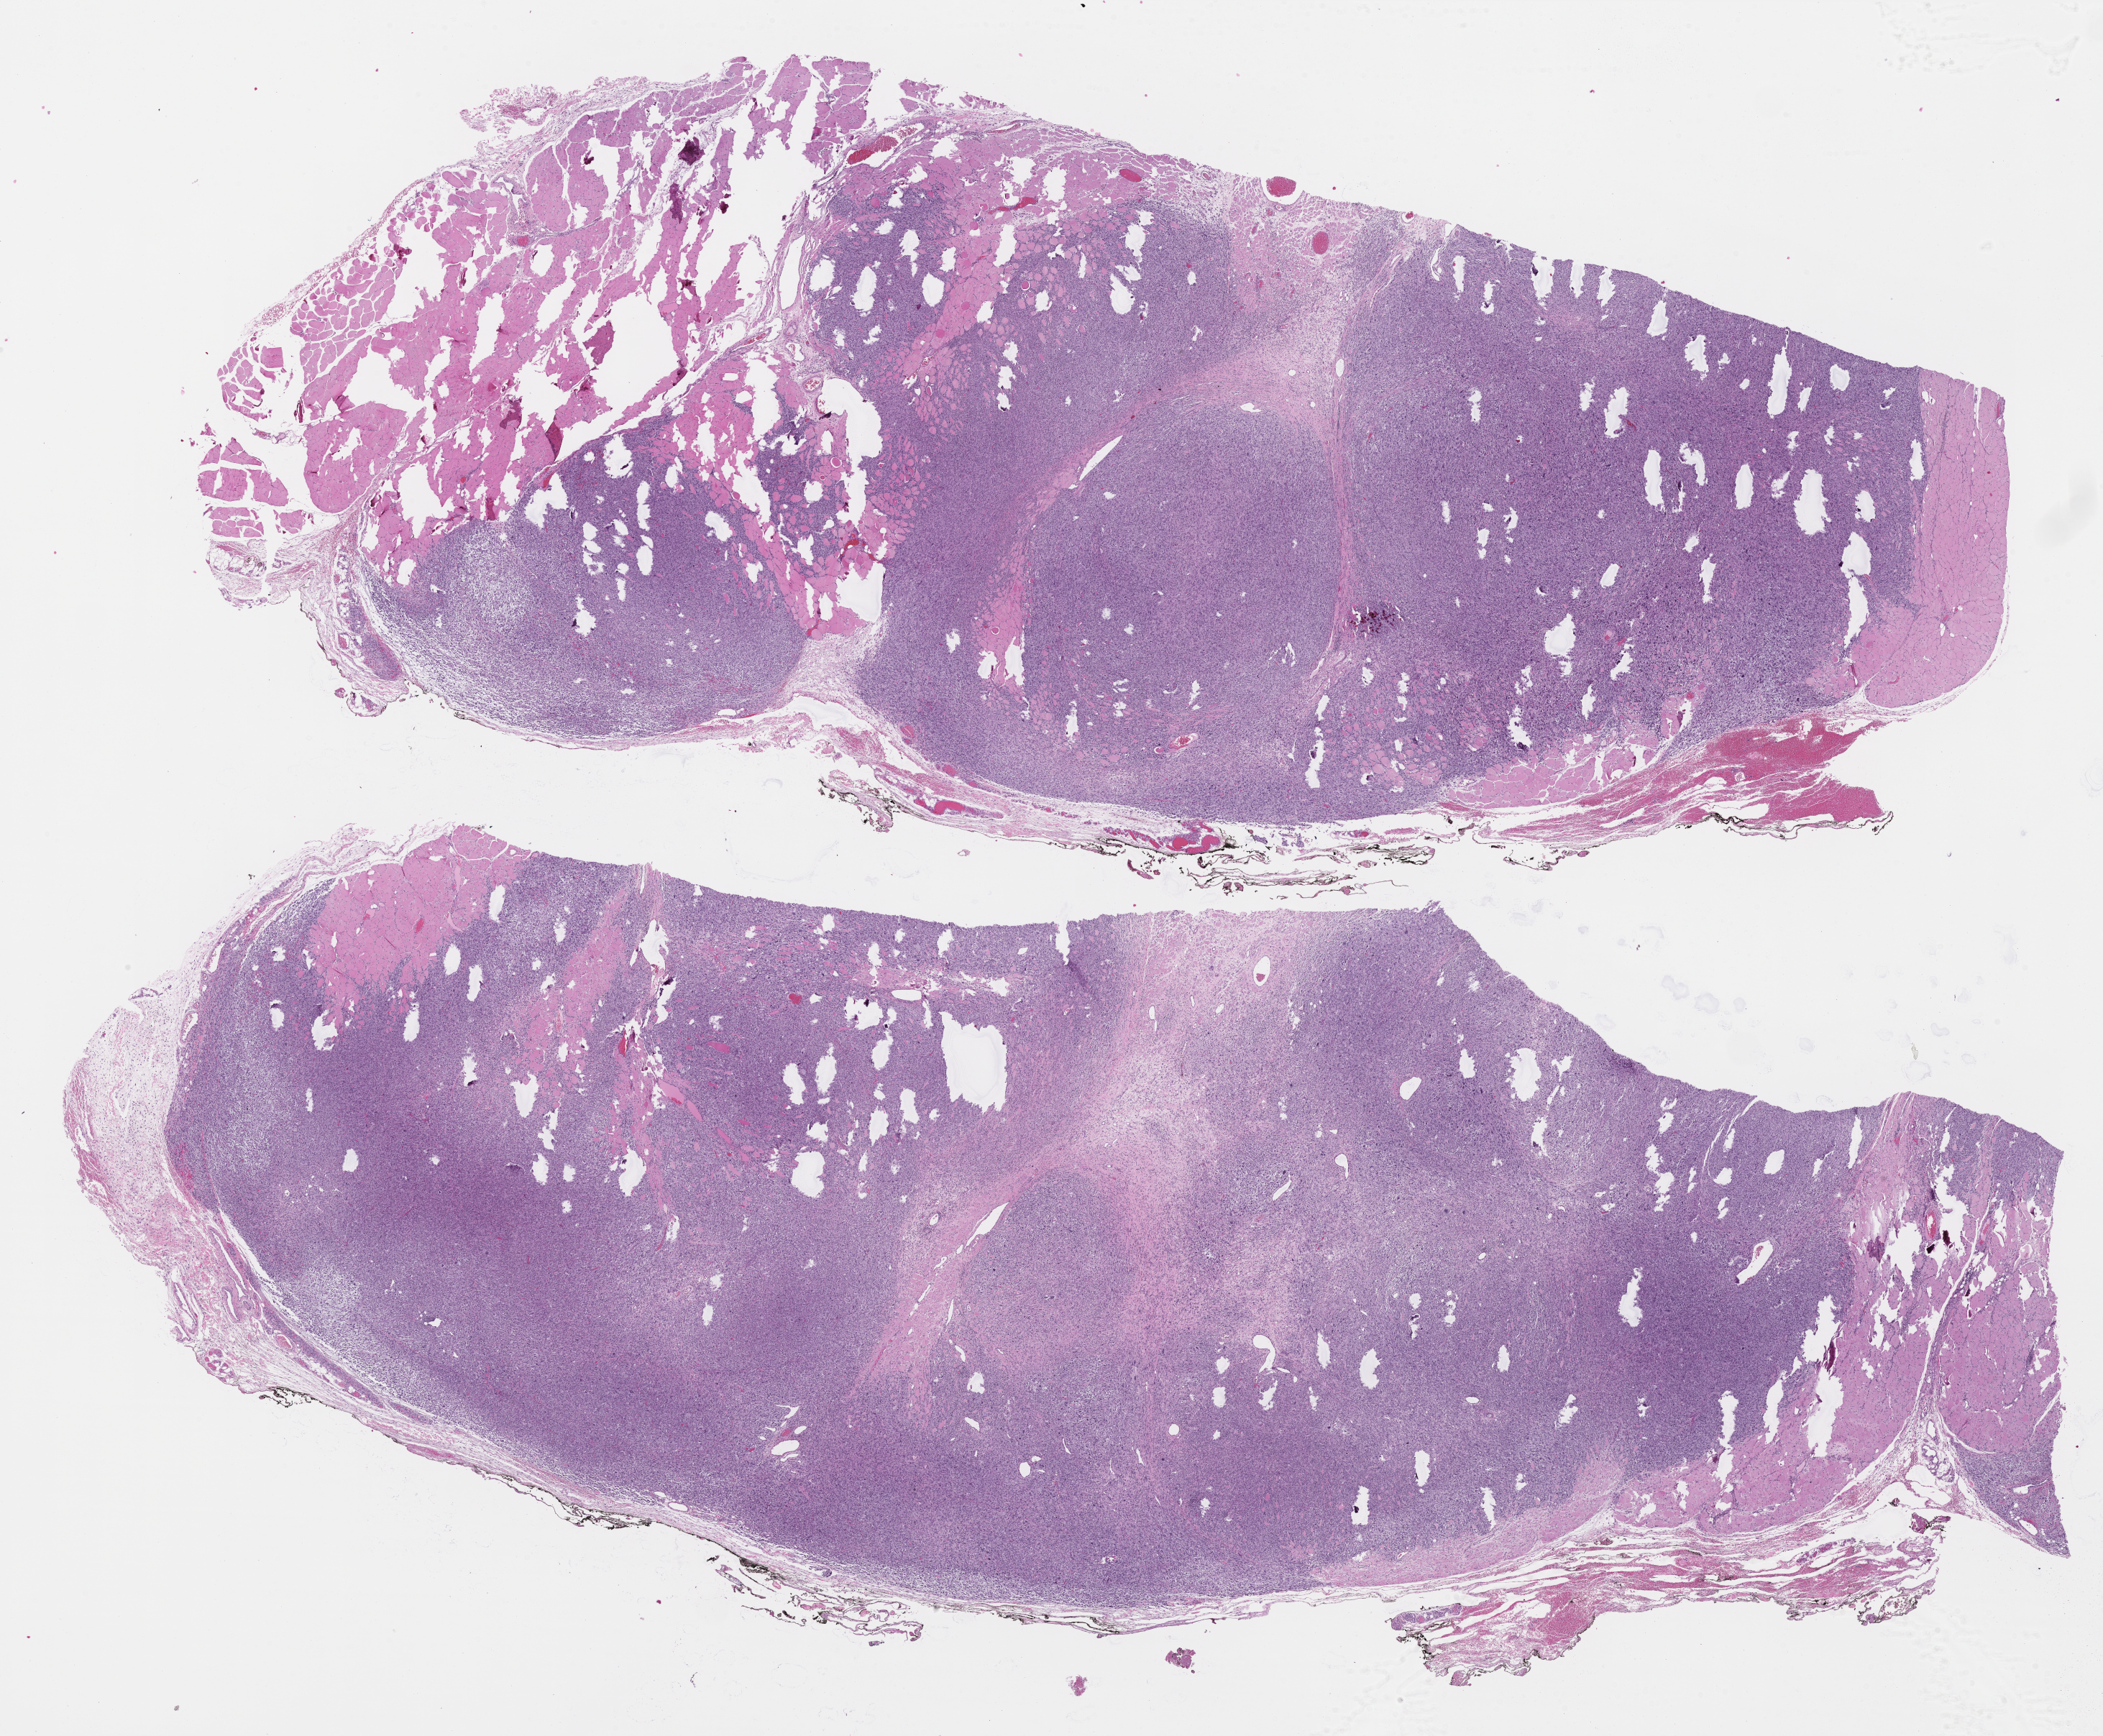
Whole-slide histology image, H&E, a low-resolution overview of the entire scanned area, about 23.5 x 19.4 mm (from a 40x scan); FFPE section; primary tumour sample from the connective, subcutaneous and other soft tissues. Male, age 86 years at initial diagnosis.
Diagnosis: Undifferentiated sarcoma (connective, subcutaneous and other soft tissues of trunk, NOS).